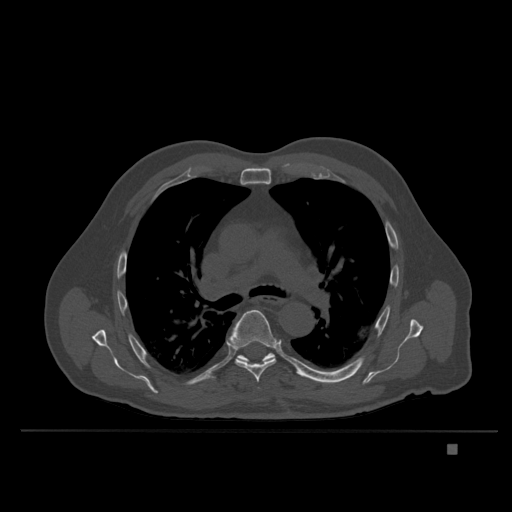
CT including the spine, one axial slice; slice 256 of 435 in the series (ordered by position); bone window (W 1800 / L 400 HU); 1.5 mm slice thickness; 512 × 512 image matrix, field of view 434 × 434 mm. Male patient, age 73 years. From the clinical record (not read from this slice): primary cancer: skin.
Outlined on this slice (semi-automatically segmented with operator editing):
- T6 vertebra: box from (x=228, y=310) to (x=276, y=383) px
- T7 vertebra: (x=235, y=353)–(x=291, y=372)